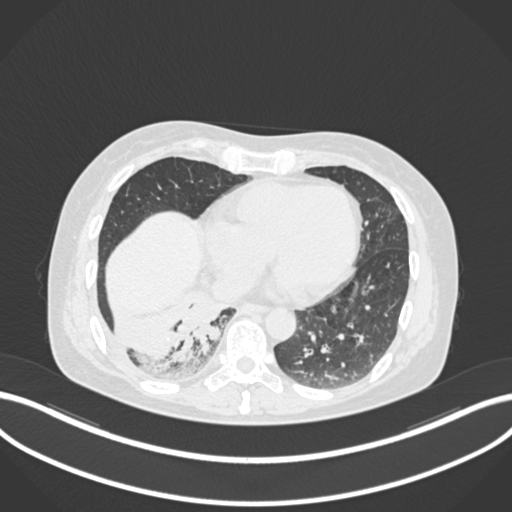
Chest CT, one axial slice. Slice 44 of 168 in the series (ordered by position). Reconstruction kernel B30f. 120 kVp. Lung window (W 1500 / L -600 HU). 1 mm slice thickness. 512 × 512 image matrix, field of view 400 × 400 mm. Female patient, age 63 years. Case-level facts recorded for this patient, not image findings: clinical TNM (as recorded): T1c N0 M0.
Structures marked on this image (bounding box drawn by a radiologist):
- lung tumour (recorded histology: adenocarcinoma): bounding box (x1, y1, x2, y2) in pixels: (172, 296, 231, 366)